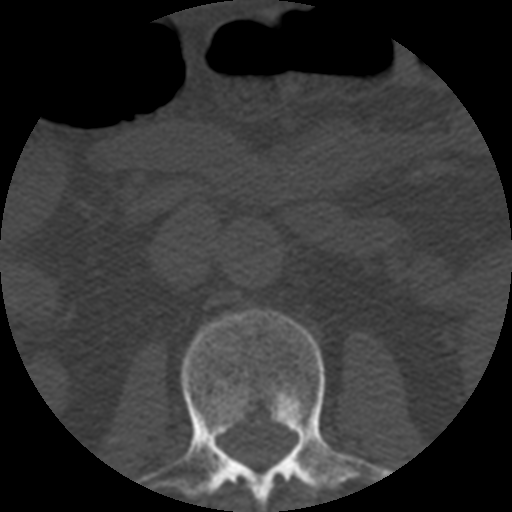
CT including the spine, one axial slice. Position 153 of 508 along the scan axis. Reconstruction kernel STANDARD. 120 kVp. Bone window (W 1800 / L 400 HU). 512 × 512 image matrix, field of view 160 × 160 mm. Patient age 57 years. Case-level facts recorded for this patient, not image findings: primary cancer: prostate.
Structures marked on this image (semi-automatically segmented with operator editing):
- L2 vertebra: bounding box [x1, y1, x2, y2] px = [137, 310, 392, 512]